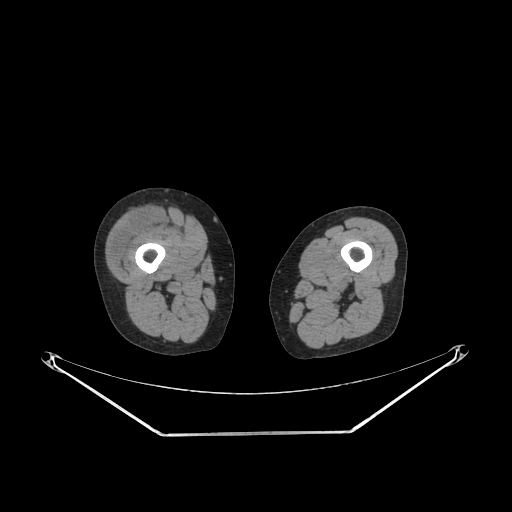
CT of an extremity soft-tissue mass (from a PET/CT study), one axial slice; slice 215 of 311 in the series (ordered by position); reconstruction kernel SOFT; 140 kVp; soft-tissue window (W 400 / L 40 HU); 3.75 mm slice thickness; 512 × 512 image matrix, field of view 500 × 500 mm. Female patient. From the clinical record (not read from this slice): histological type: pleiomorphic undifferentiated sarcoma; grade: high; site of the primary tumour: right quadricep.
Annotated regions visible in this slice (expert contour drawn on MRI and transferred to this co-registered scan by the dataset authors):
- tumour plus oedema (research contour): bounding box (x1, y1, x2, y2) in pixels: (110, 210, 161, 263)